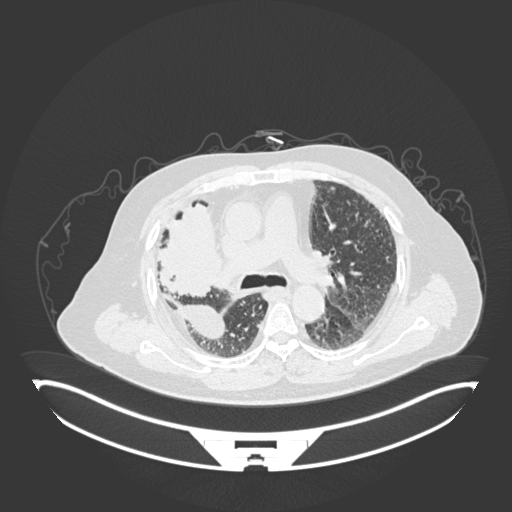
Chest CT, one axial slice. Position 108 of 201 along the scan axis. Reconstruction kernel B30f. Lung window (W 1500 / L -600 HU). 1 mm slice thickness. 512 × 512 image matrix, field of view 500 × 500 mm. Male patient, age 69 years. From the clinical record (not read from this slice): clinical TNM (as recorded): T4 N3 M1.
Outlined on this slice (rectangle marked by the reading radiologist):
- lung tumour (recorded histology: adenocarcinoma): bounding box (x1, y1, x2, y2) in pixels: (158, 200, 230, 297)